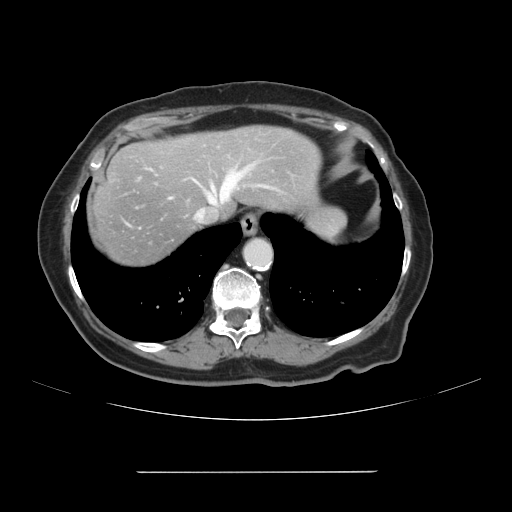
Contrast-enhanced abdominal CT, one axial slice; slice 93 of 111 in the series (ordered by position); intravenous contrast given; soft-tissue window (W 400 / L 40 HU); 512 × 512 image matrix, field of view 400 × 400 mm. Female patient, age 74 years. From the clinical record (not read from this slice): diagnosis: colorectal cancer liver metastases, imaged before liver resection; multiple liver metastases: yes; largest metastasis: 1.1 cm; disease in both lobes: yes.
Structures marked on this image (manually delineated by an expert):
- hepatic veins: box from (x=197, y=169) to (x=249, y=217) px
- liver: (x=91, y=125)–(x=321, y=268)
- planned liver remnant (the part of the liver to remain after resection): (x=177, y=126)–(x=321, y=214)
- portal vein (with intrahepatic branches): (x=211, y=191)–(x=220, y=200)
- liver metastasis: (x=110, y=174)–(x=117, y=180)